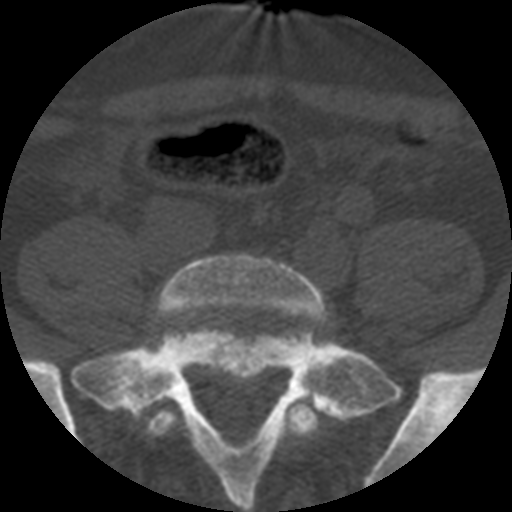
CT including the spine, one axial slice; reconstruction kernel STANDARD; 120 kVp; bone window (W 1800 / L 400 HU); 1.25 mm slice thickness; 512 × 512 image matrix, field of view 160 × 160 mm. Patient age 57 years. From the clinical record (not read from this slice): primary cancer: prostate.
Structures marked on this image (semi-automatic segmentation, software-assisted and operator-edited):
- L5 vertebra: bounding box <145,254,329,438> (left, top, right, bottom; pixels)